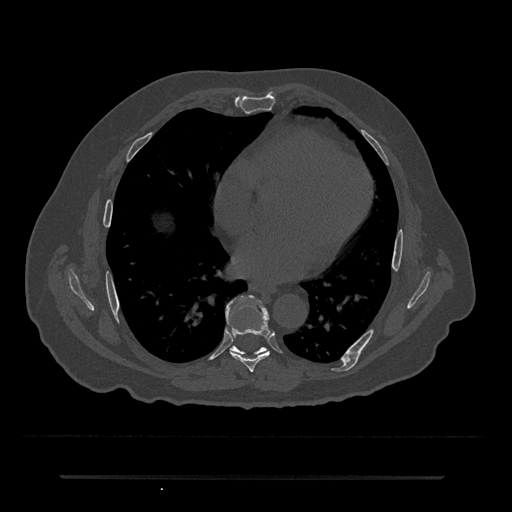
CT including the spine, one axial slice; position 367 of 797 along the scan axis; reconstruction kernel Br40s/3; 120 kVp; bone window (W 1800 / L 400 HU); 512 × 512 image matrix, field of view 437 × 437 mm. Patient: male, 69 years. From the clinical record (not read from this slice): primary cancer: prostate.
Structures marked on this image (semi-automatically segmented with operator editing):
- T7 vertebra: bounding box [x1, y1, x2, y2] px = [226, 296, 271, 372]
- T8 vertebra: [230, 346, 266, 355]